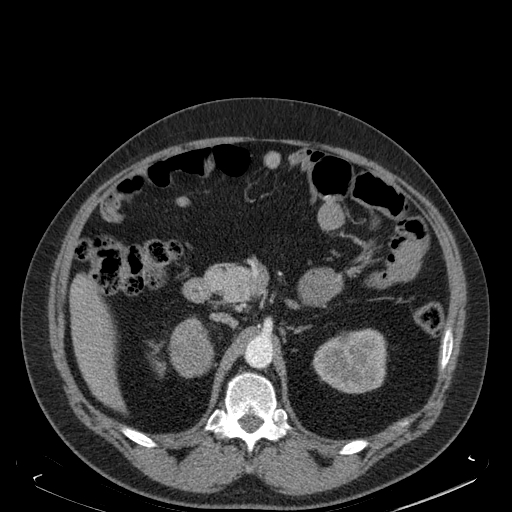
Contrast-enhanced abdominal CT, one axial slice; soft-tissue window (W 400 / L 40 HU); 1.5 mm slice thickness; 512 × 512 image matrix, field of view 405 × 405 mm. Male patient. From the clinical record (not read from this slice): diagnosis: adrenocortical carcinoma; tumour side: right adrenal; tumour size at pathology: 7.5 cm; Ki-67 index: 25 %; stage (as recorded): 4.
Structures marked on this image (semi-automatically segmented with operator editing):
- mass: bounding box <171,319,211,376> (left, top, right, bottom; pixels)